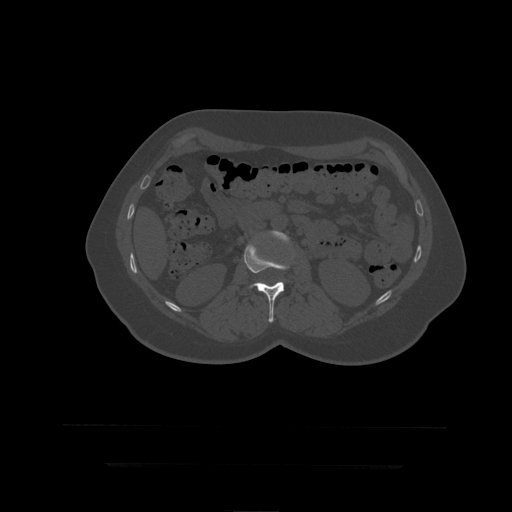
CT including the spine, one axial slice; slice 143 of 399 in the series (ordered by position); reconstruction kernel STANDARD; 120 kVp; bone window (W 1800 / L 400 HU); 1.25 mm slice thickness; 512 × 512 image matrix, field of view 450 × 450 mm. Patient age 41 years. From the clinical record (not read from this slice): primary cancer: breast.
Structures marked on this image (semi-automatic segmentation, software-assisted and operator-edited):
- L2 vertebra: bounding box (x1, y1, x2, y2) in pixels: (244, 244, 290, 323)
- L3 vertebra: (268, 231, 289, 243)